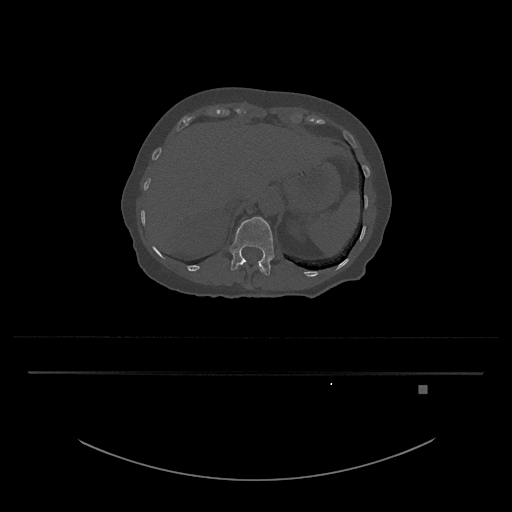
CT including the spine, one axial slice; position 571 of 797 along the scan axis; 120 kVp; bone window (W 1800 / L 400 HU); 0.5 mm slice thickness; 512 × 512 image matrix, field of view 500 × 500 mm. Patient: female, 57 years. From the clinical record (not read from this slice): primary cancer: cervical.
Annotated regions visible in this slice (semi-automatically segmented with operator editing):
- L1 vertebra: box from (x=229, y=217) to (x=275, y=276) px
- T12 vertebra: (x=235, y=262)–(x=264, y=273)